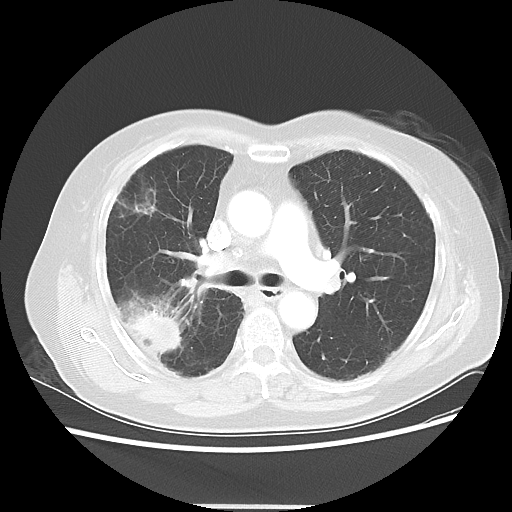
Chest CT, one axial slice; slice 30 of 50 in the series (ordered by position); lung window (W 1500 / L -600 HU); 512 × 512 image matrix. Patient: female, 72 years. From the clinical record (not read from this slice): clinical TNM (as recorded): T2 N1 M0; histopathological grade: G1.
Structures marked on this image (bounding box drawn by a radiologist):
- lung tumour (recorded histology: adenocarcinoma): bounding box [x1, y1, x2, y2] px = [129, 304, 184, 354]